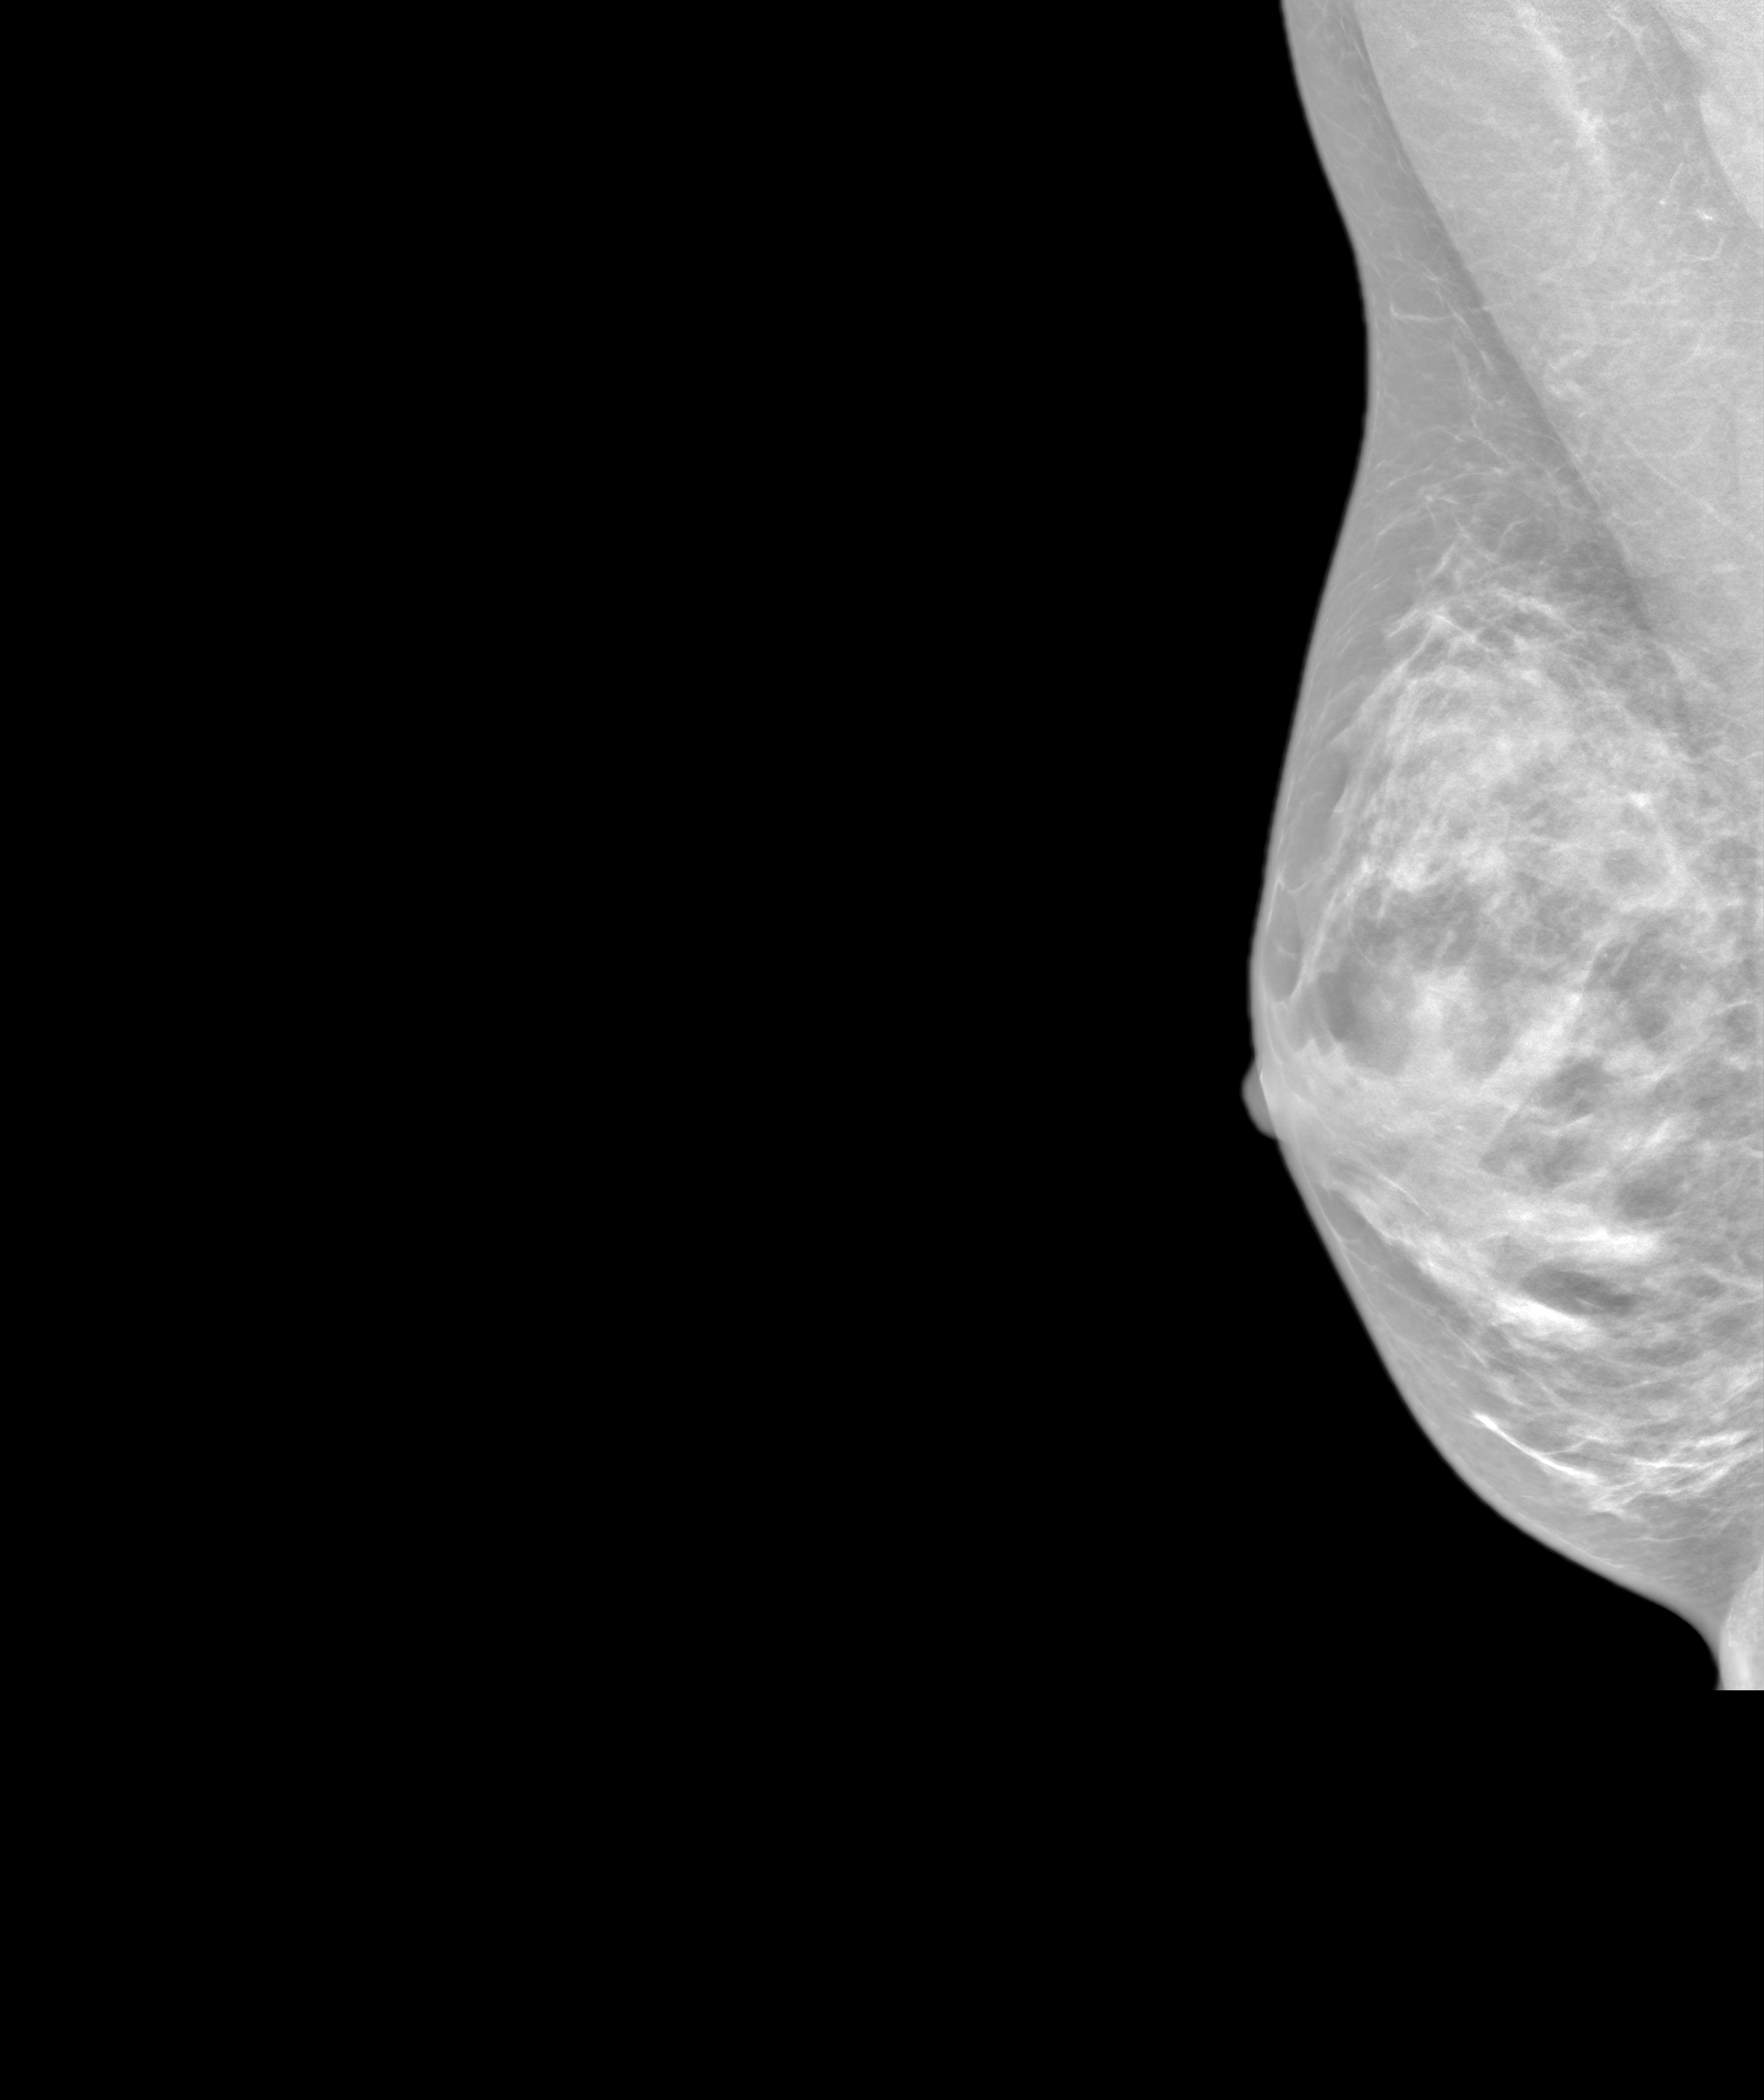
Annual screening mammography examination. Patient aged 44 years (female).
Image type: synthesized 2-D view from tomosynthesis. Breast: right. Projection: MLO view.